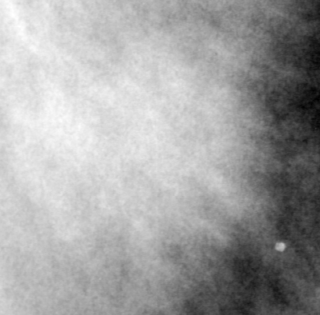
Cropped region of a digitized screen-film mammogram centred on a radiologist-marked abnormality, right breast, MLO view, BI-RADS breast density category 4 (scale 1–4).
Finding: mass, shape irregular, margins ill defined; BI-RADS assessment category 4; pathology result (as recorded, not read from the image): benign.